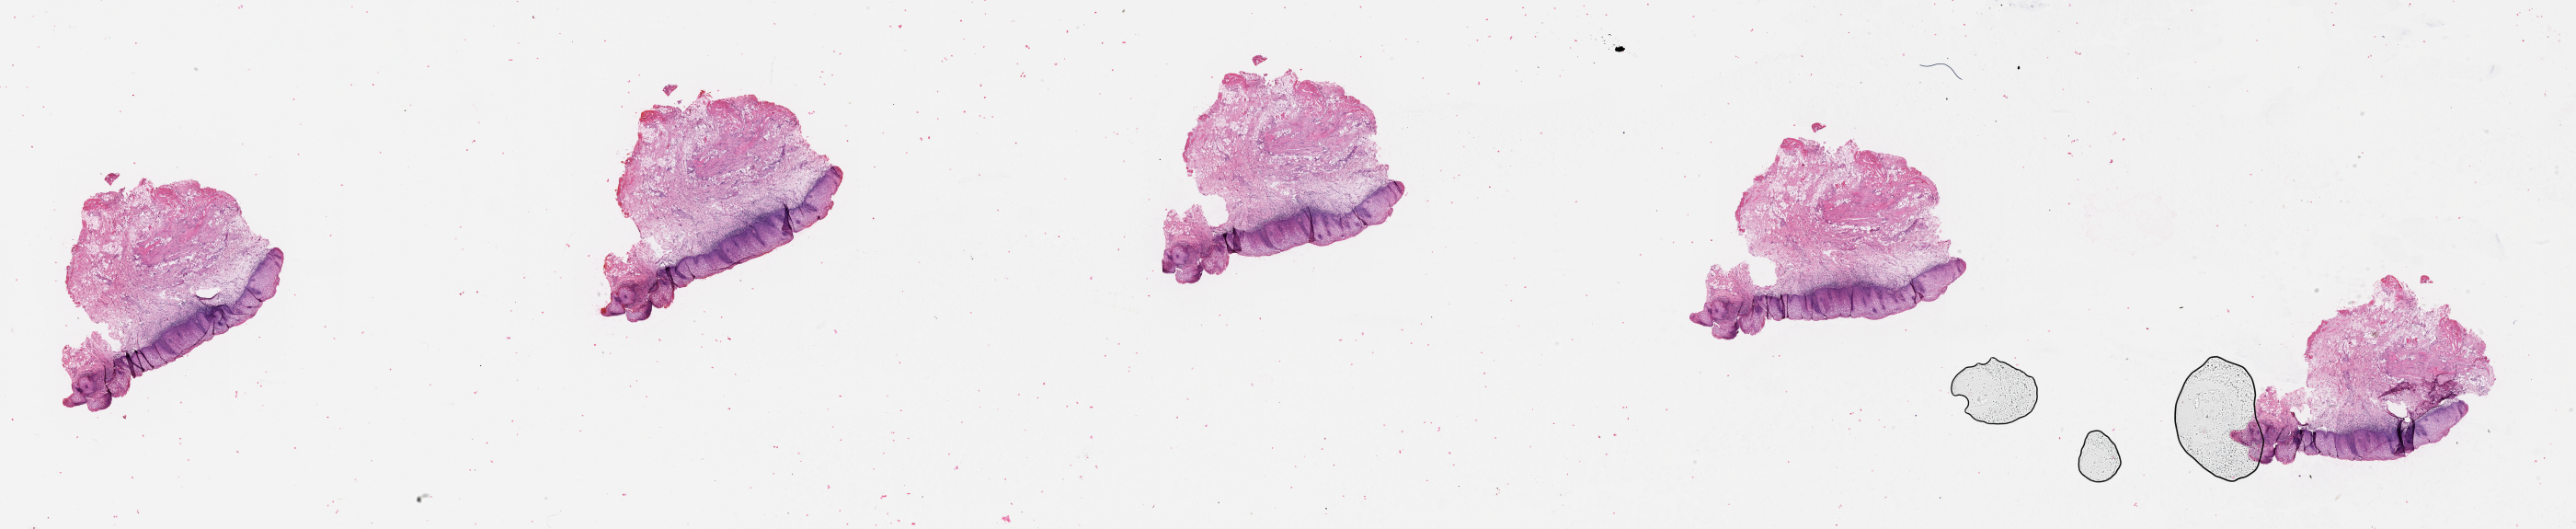
Whole-slide histology image, Hematoxylin and eosin (H&E) stained — shown as a low-resolution overview of the whole scanned area (about 45.1 x 9.3 mm); normal (non-tumour) tissue sample, sampled site: buccal mucosa. Male, 69 y/o.
• this section: normal (non-tumour) tissue from the same patient
• patient diagnosis: Squamous cell carcinoma, NOS (cheek mucosa)